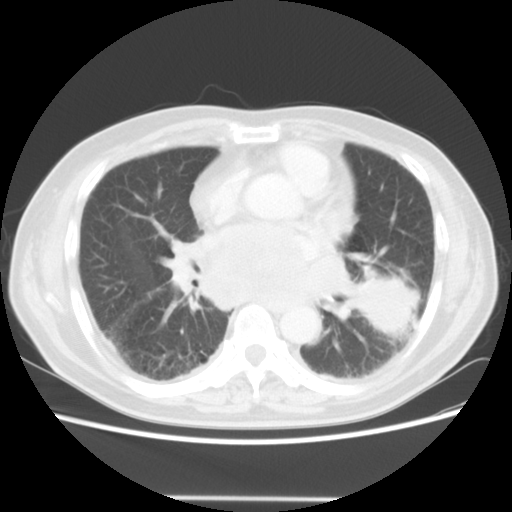
Chest CT, one axial slice; position 24 of 56 along the scan axis; reconstruction kernel STANDARD; 140 kVp; lung window (W 1500 / L -600 HU); 512 × 512 image matrix. Male patient, age 66 years. Case-level facts recorded for this patient, not image findings: clinical TNM (as recorded): T4 N3 M0.
Structures marked on this image (bounding box drawn by a radiologist):
- lung tumour (recorded histology: small cell carcinoma): box from (x=347, y=259) to (x=419, y=336) px